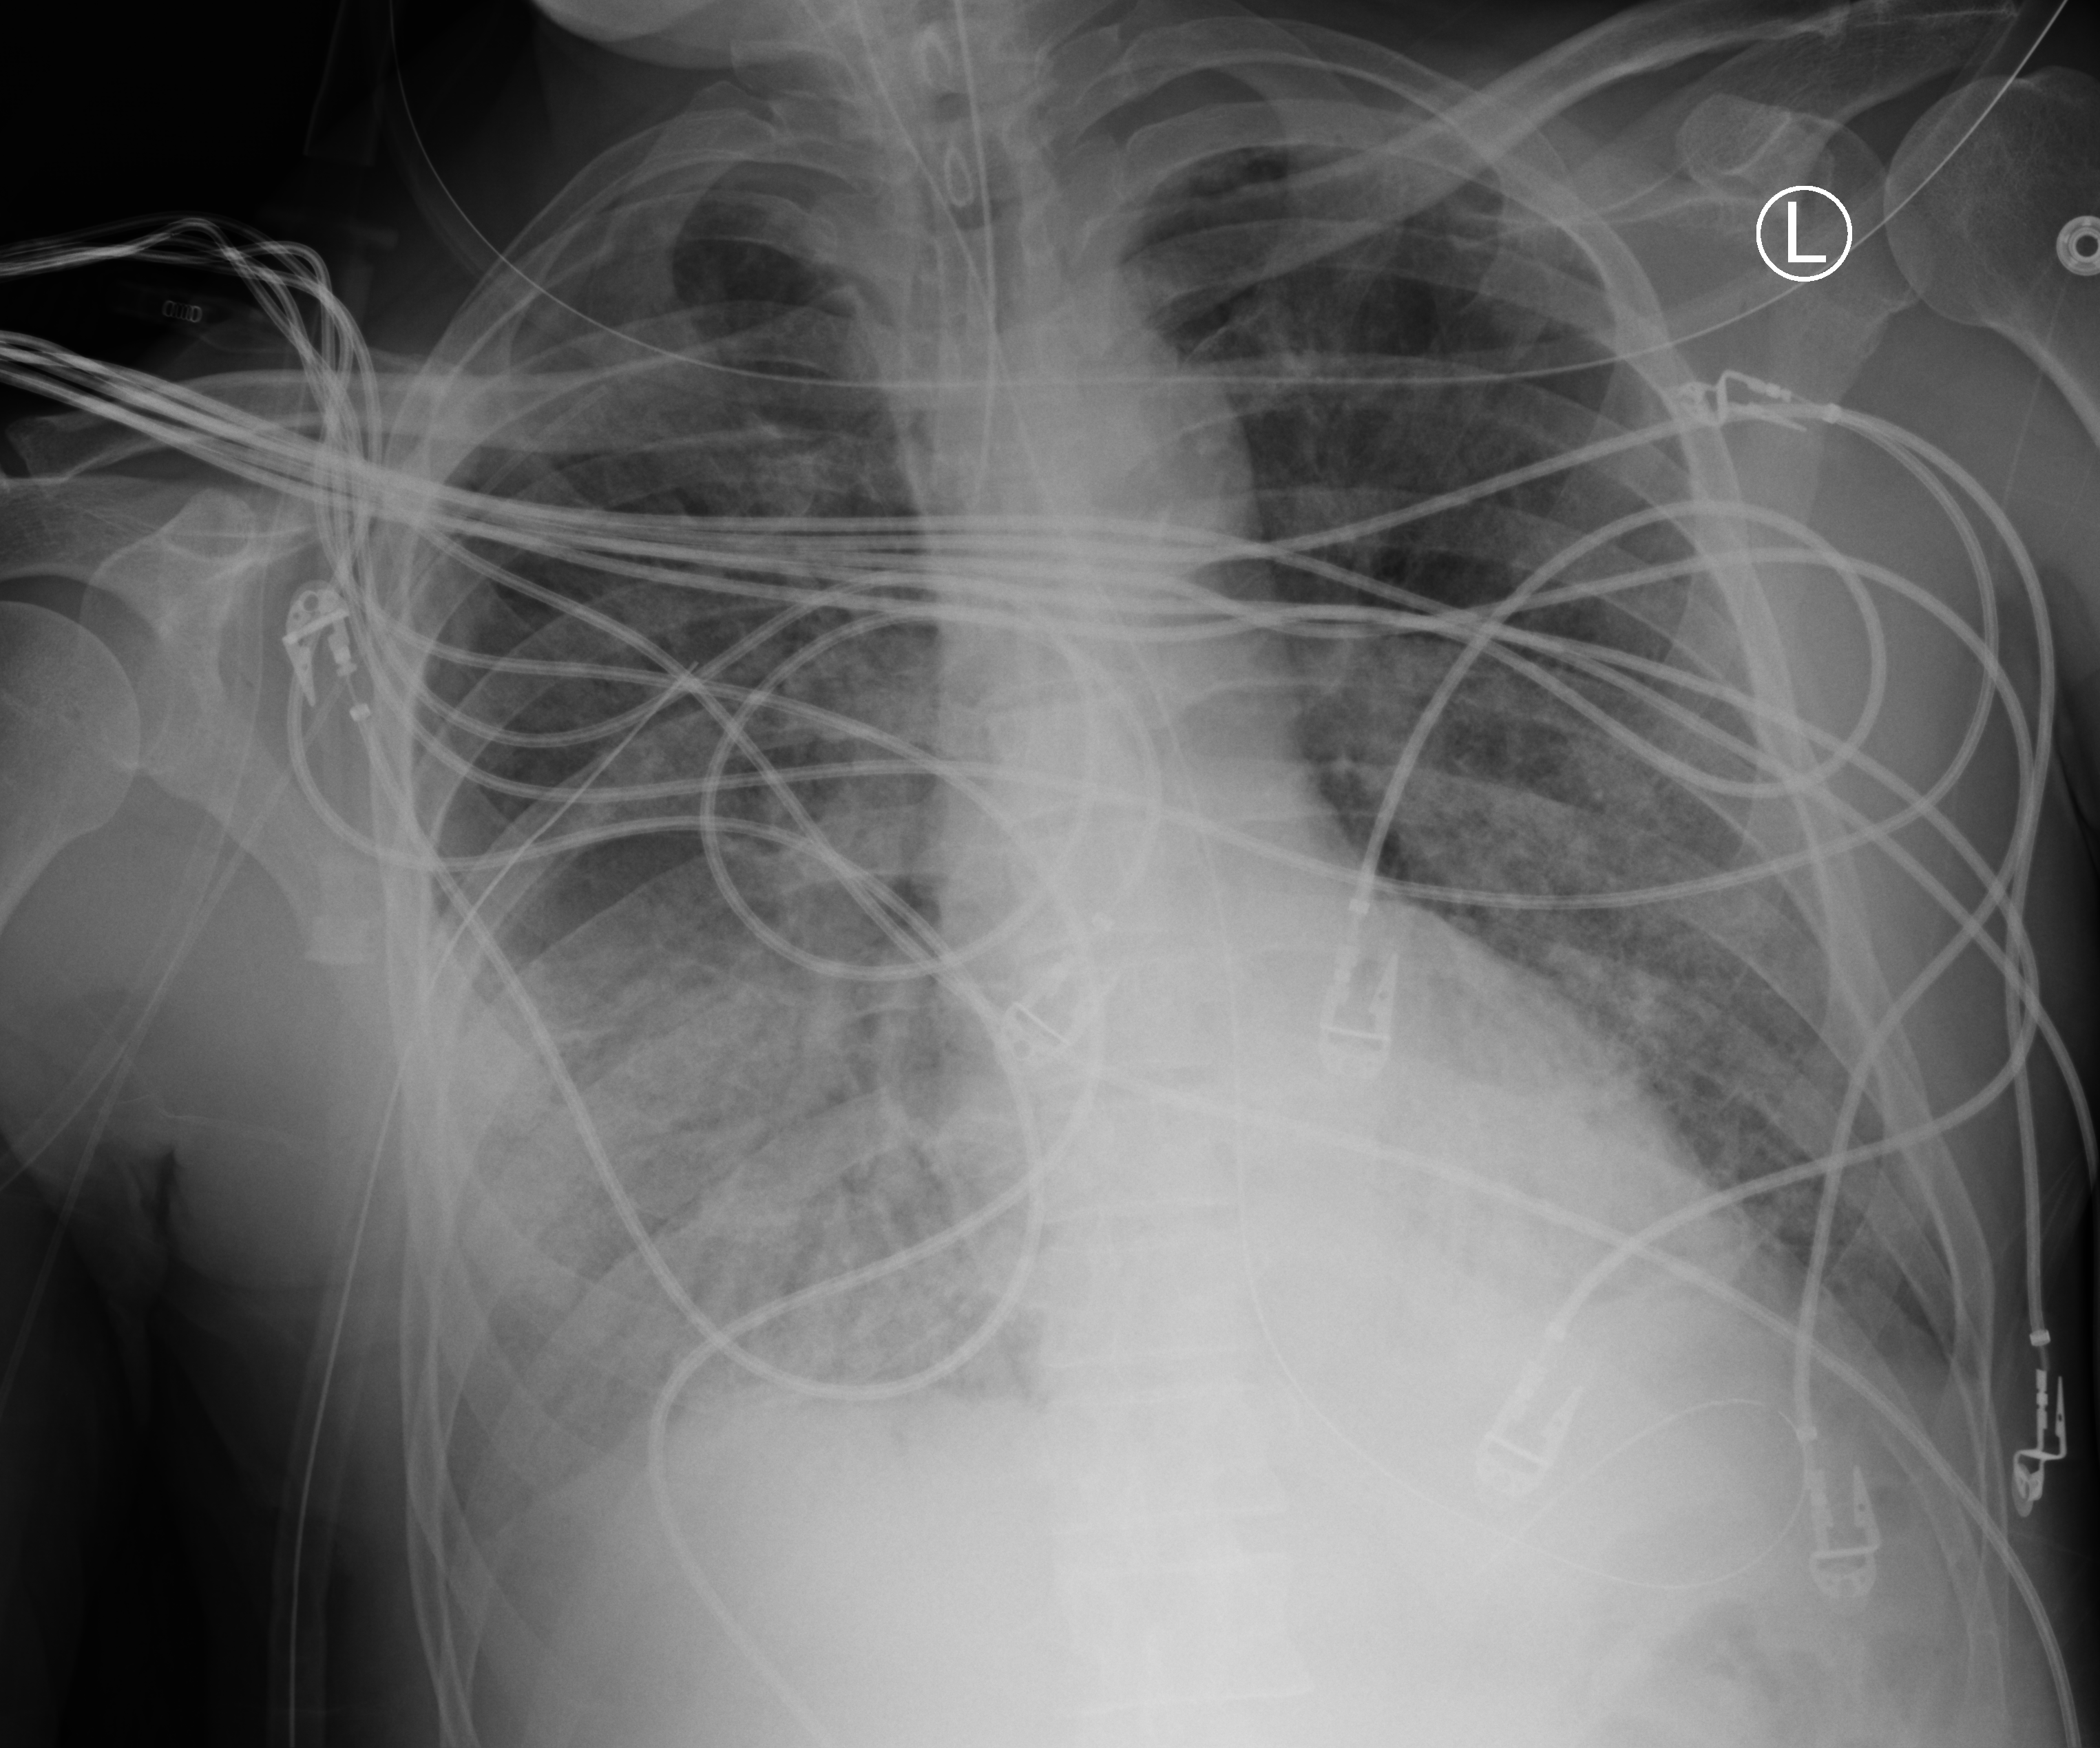
Bedside chest radiograph (computed radiography), anteroposterior (AP) projection. Male patient hospitalised with COVID-19, age 60–74 years.
Hospital-stay facts (about this admission, not read from this image; timing relative to this image not recorded):
- hypertension (admission record): no
- mechanically ventilated during this hospital stay: yes